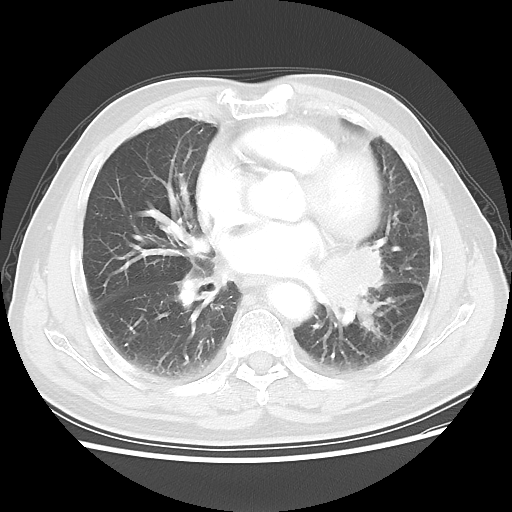
Chest CT, one axial slice; slice 28 of 56 in the series (ordered by position); reconstruction kernel LUNG; 120 kVp; lung window (W 1500 / L -600 HU); 5 mm slice thickness; 512 × 512 image matrix, field of view 360 × 360 mm. Patient: male, 75 years. From the clinical record (not read from this slice): clinical TNM (as recorded): T3 N0 M0.
Structures marked on this image (bounding box drawn by a radiologist):
- lung tumour (recorded histology: squamous cell carcinoma): bounding box (x1, y1, x2, y2) in pixels: (306, 242, 387, 320)